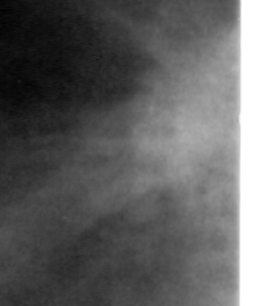
Cropped region of a digitized screen-film mammogram centred on a radiologist-marked abnormality, left breast, CC view, BI-RADS breast density category 4 (scale 1–4).
Finding: mass, shape irregular, margins spiculated; BI-RADS assessment category 4; pathology result (as recorded, not read from the image): malignant.